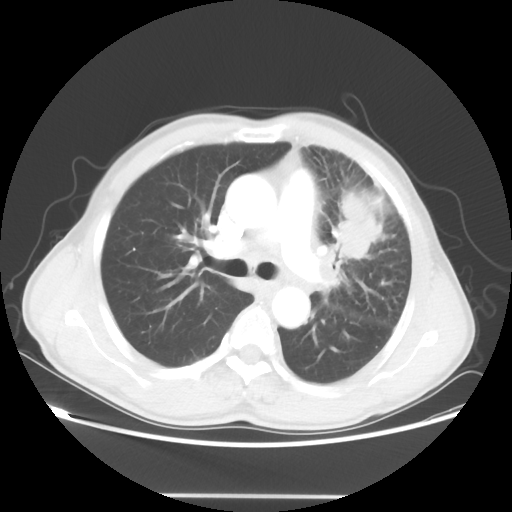
Chest CT, one axial slice; position 33 of 55 along the scan axis; lung window (W 1500 / L -600 HU); 5 mm slice thickness; 512 × 512 image matrix, field of view 398 × 398 mm. Patient: male, 60 years. From the clinical record (not read from this slice): clinical TNM (as recorded): T3 N3 M0.
Annotated regions visible in this slice (rectangle marked by the reading radiologist):
- lung tumour (recorded histology: adenocarcinoma): bounding box (x1, y1, x2, y2) in pixels: (334, 189, 389, 265)